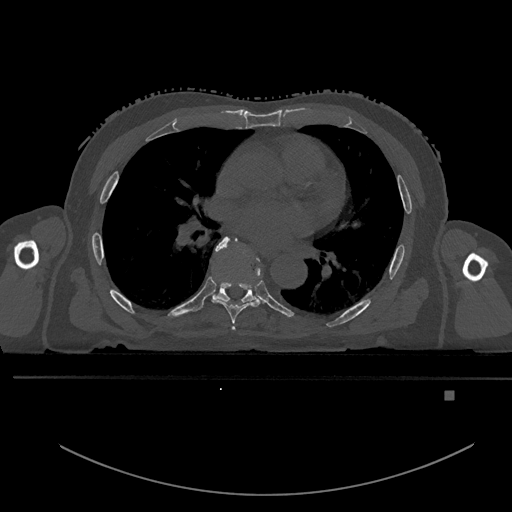
CT including the spine, one axial slice. Bone window (W 1800 / L 400 HU). 0.5 mm slice thickness. 512 × 512 image matrix. Patient: male, 82 years. Case-level facts recorded for this patient, not image findings: primary cancer: prostate; vertebrae with lytic lesions (as recorded): T11, T9, T8, T2.
Annotated regions visible in this slice (semi-automatic segmentation, software-assisted and operator-edited):
- T5 vertebra: box from (x=232, y=326) to (x=235, y=331) px
- T6 vertebra: (x=211, y=236)–(x=260, y=324)
- T7 vertebra: (x=214, y=282)–(x=256, y=302)